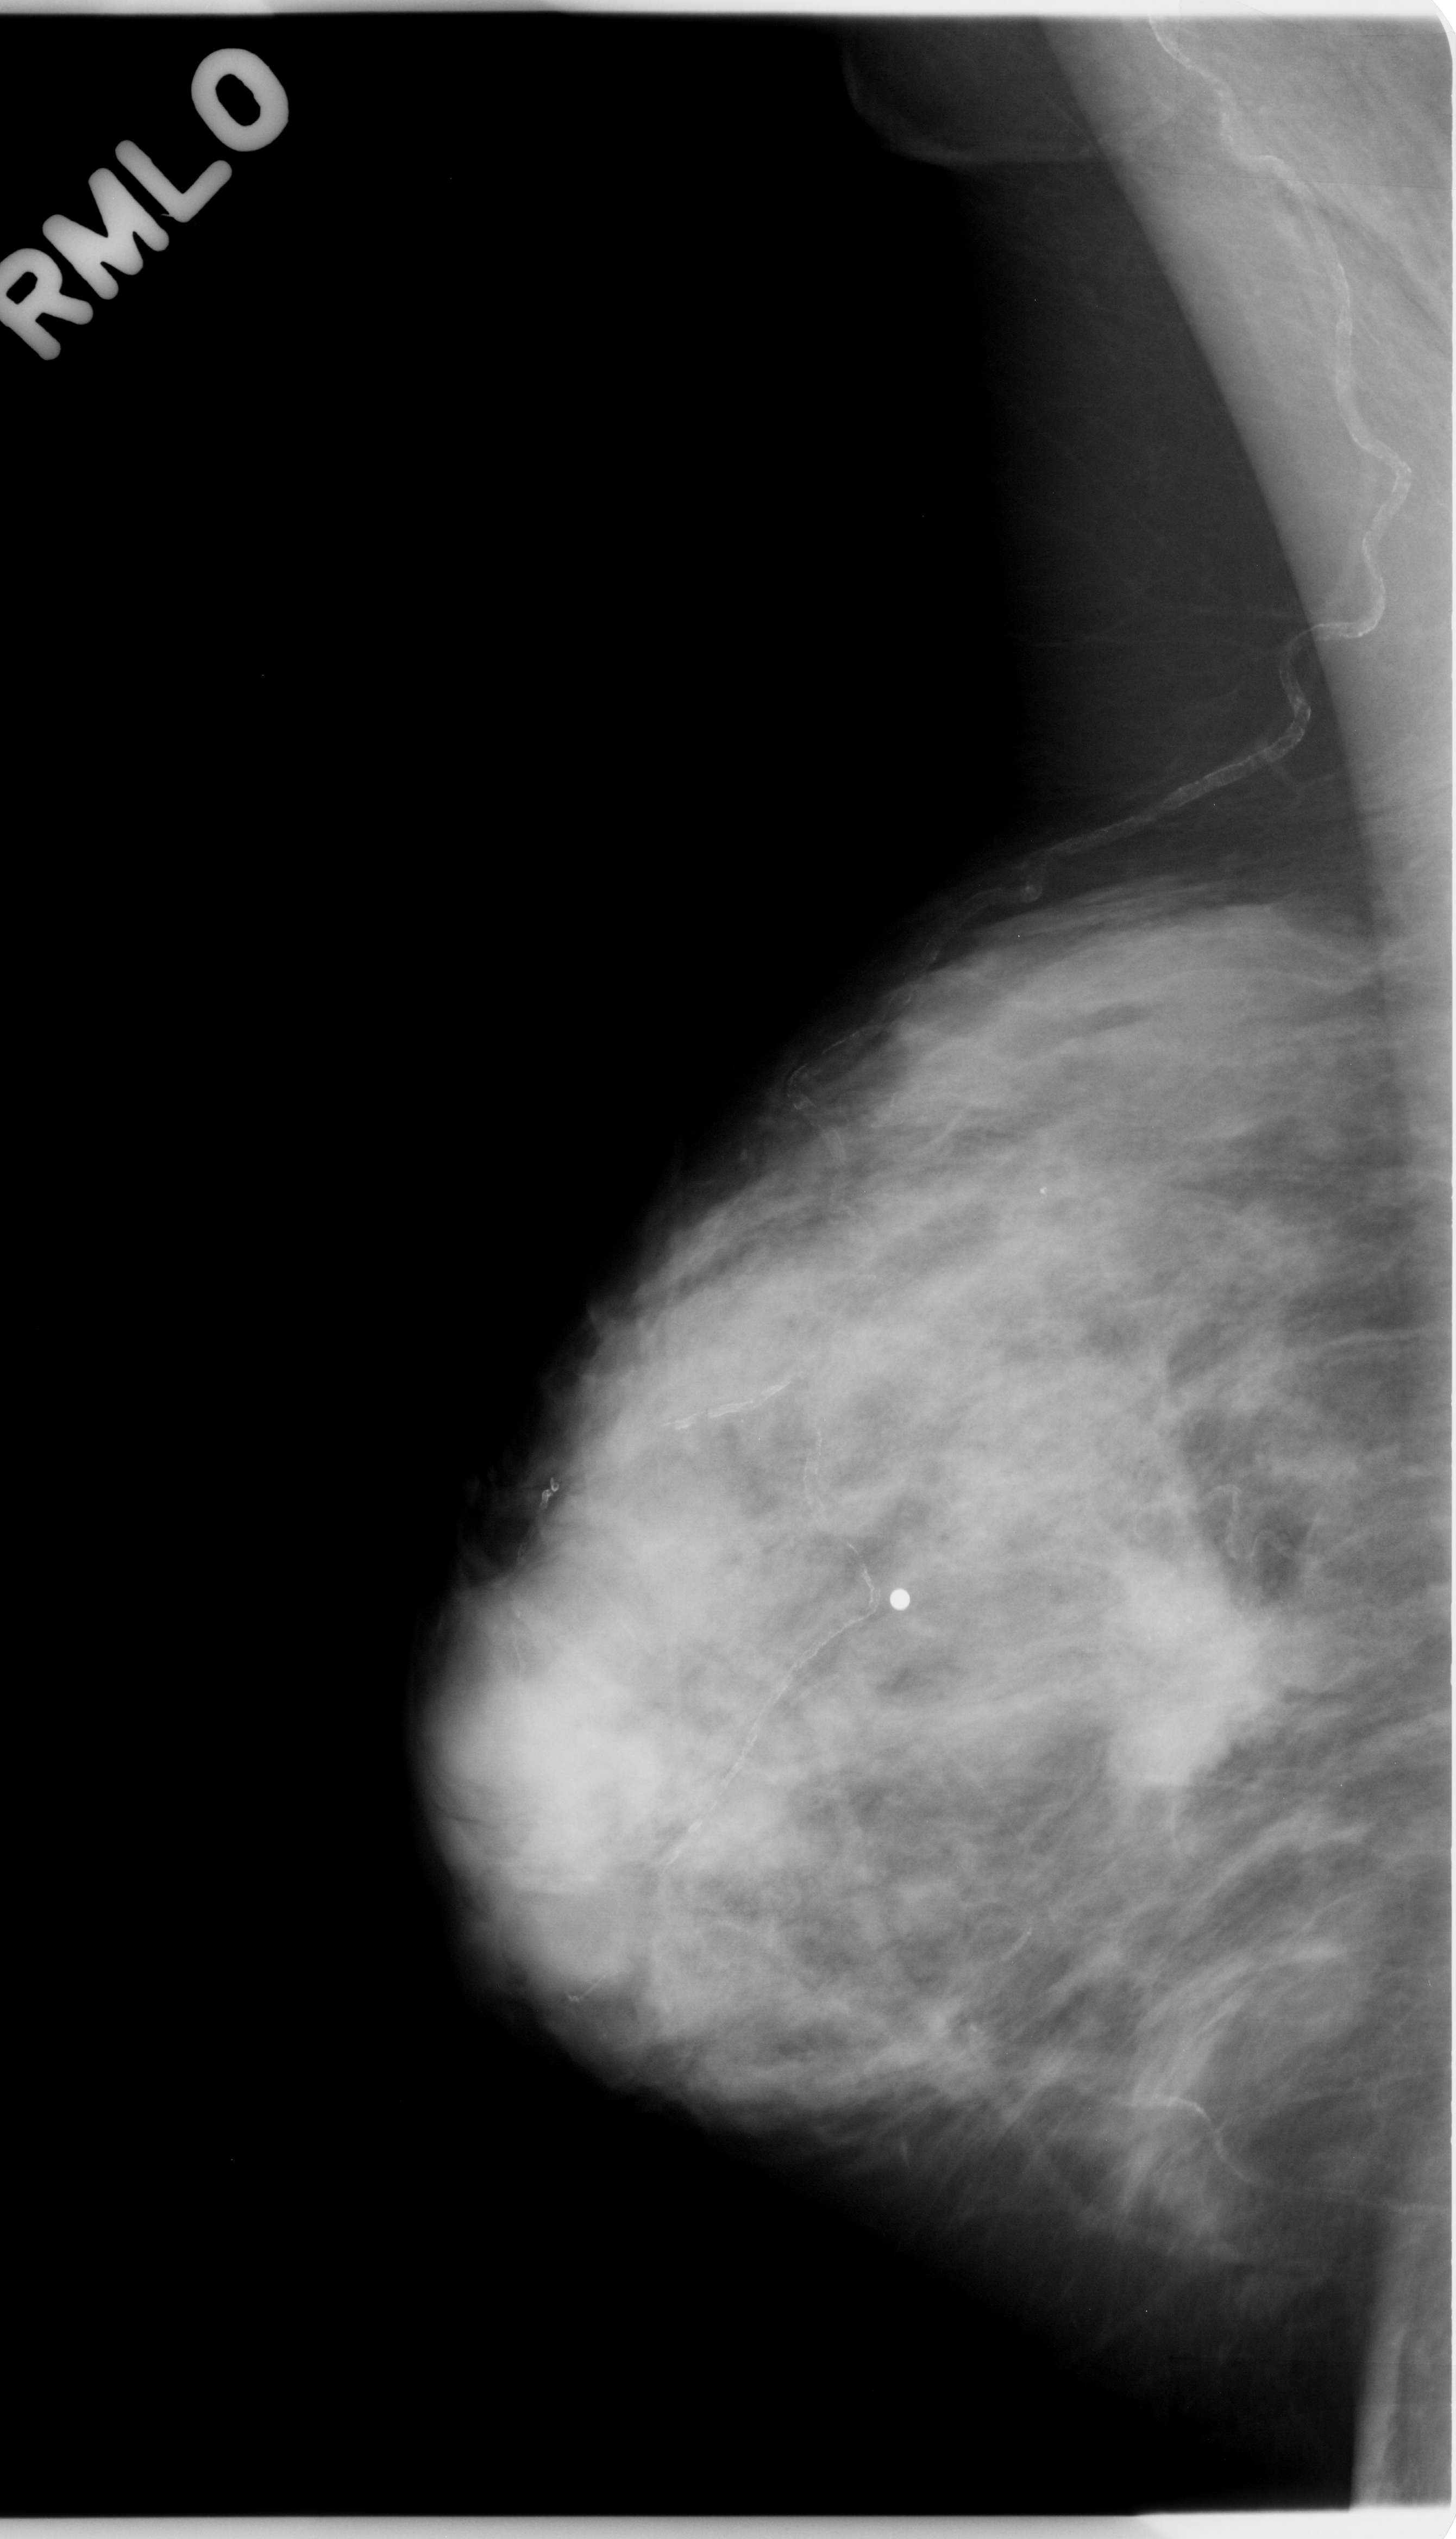
Mammogram (digitized film); right breast; mediolateral oblique (MLO) view; breast composition: heterogeneously dense (BI-RADS density category 3 of 4); 1456 × 2539 image matrix.
Expert-marked regions of interest on this image (one box per marked abnormality):
- calcifications, morphology amorphous, distribution clustered; BI-RADS assessment category 5; subtlety rating 5 on a 1 (subtle) to 5 (obvious) scale; pathology result (as recorded, not read from the image): malignant: box from (x=969, y=1347) to (x=1392, y=1910) px